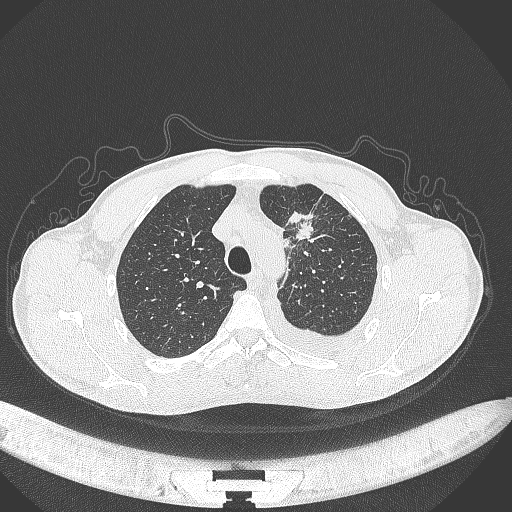
Chest CT, one axial slice; position 267 of 371 along the scan axis; reconstruction kernel B70f; lung window (W 1500 / L -600 HU); 1 mm slice thickness; 512 × 512 image matrix, field of view 400 × 400 mm. Male patient, age 49 years. Case-level facts recorded for this patient, not image findings: clinical TNM (as recorded): T1c N1 M1.
Annotated regions visible in this slice (bounding box drawn by a radiologist):
- lung tumour (recorded histology: adenocarcinoma): box from (x=283, y=209) to (x=321, y=243) px